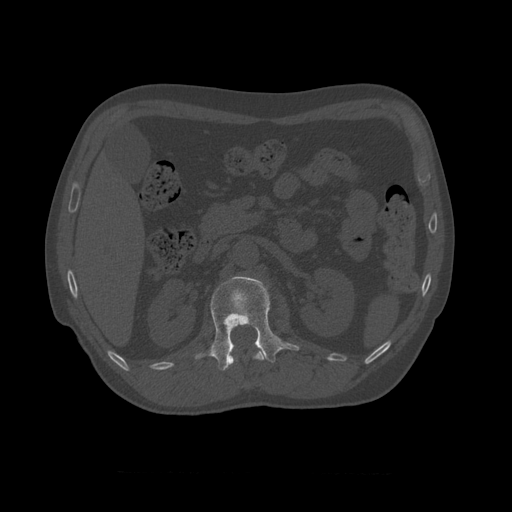
CT including the spine, one axial slice; reconstruction kernel STANDARD; bone window (W 1800 / L 400 HU); 512 × 512 image matrix, field of view 405 × 405 mm. Patient age 75 years. From the clinical record (not read from this slice): primary cancer: prostate.
Structures marked on this image (semi-automatically segmented with operator editing):
- L1 vertebra: box from (x=194, y=276) to (x=300, y=371) px
- T10 vertebra: (x=223, y=342)–(x=265, y=370)
- T11 vertebra: (x=226, y=353)–(x=265, y=370)